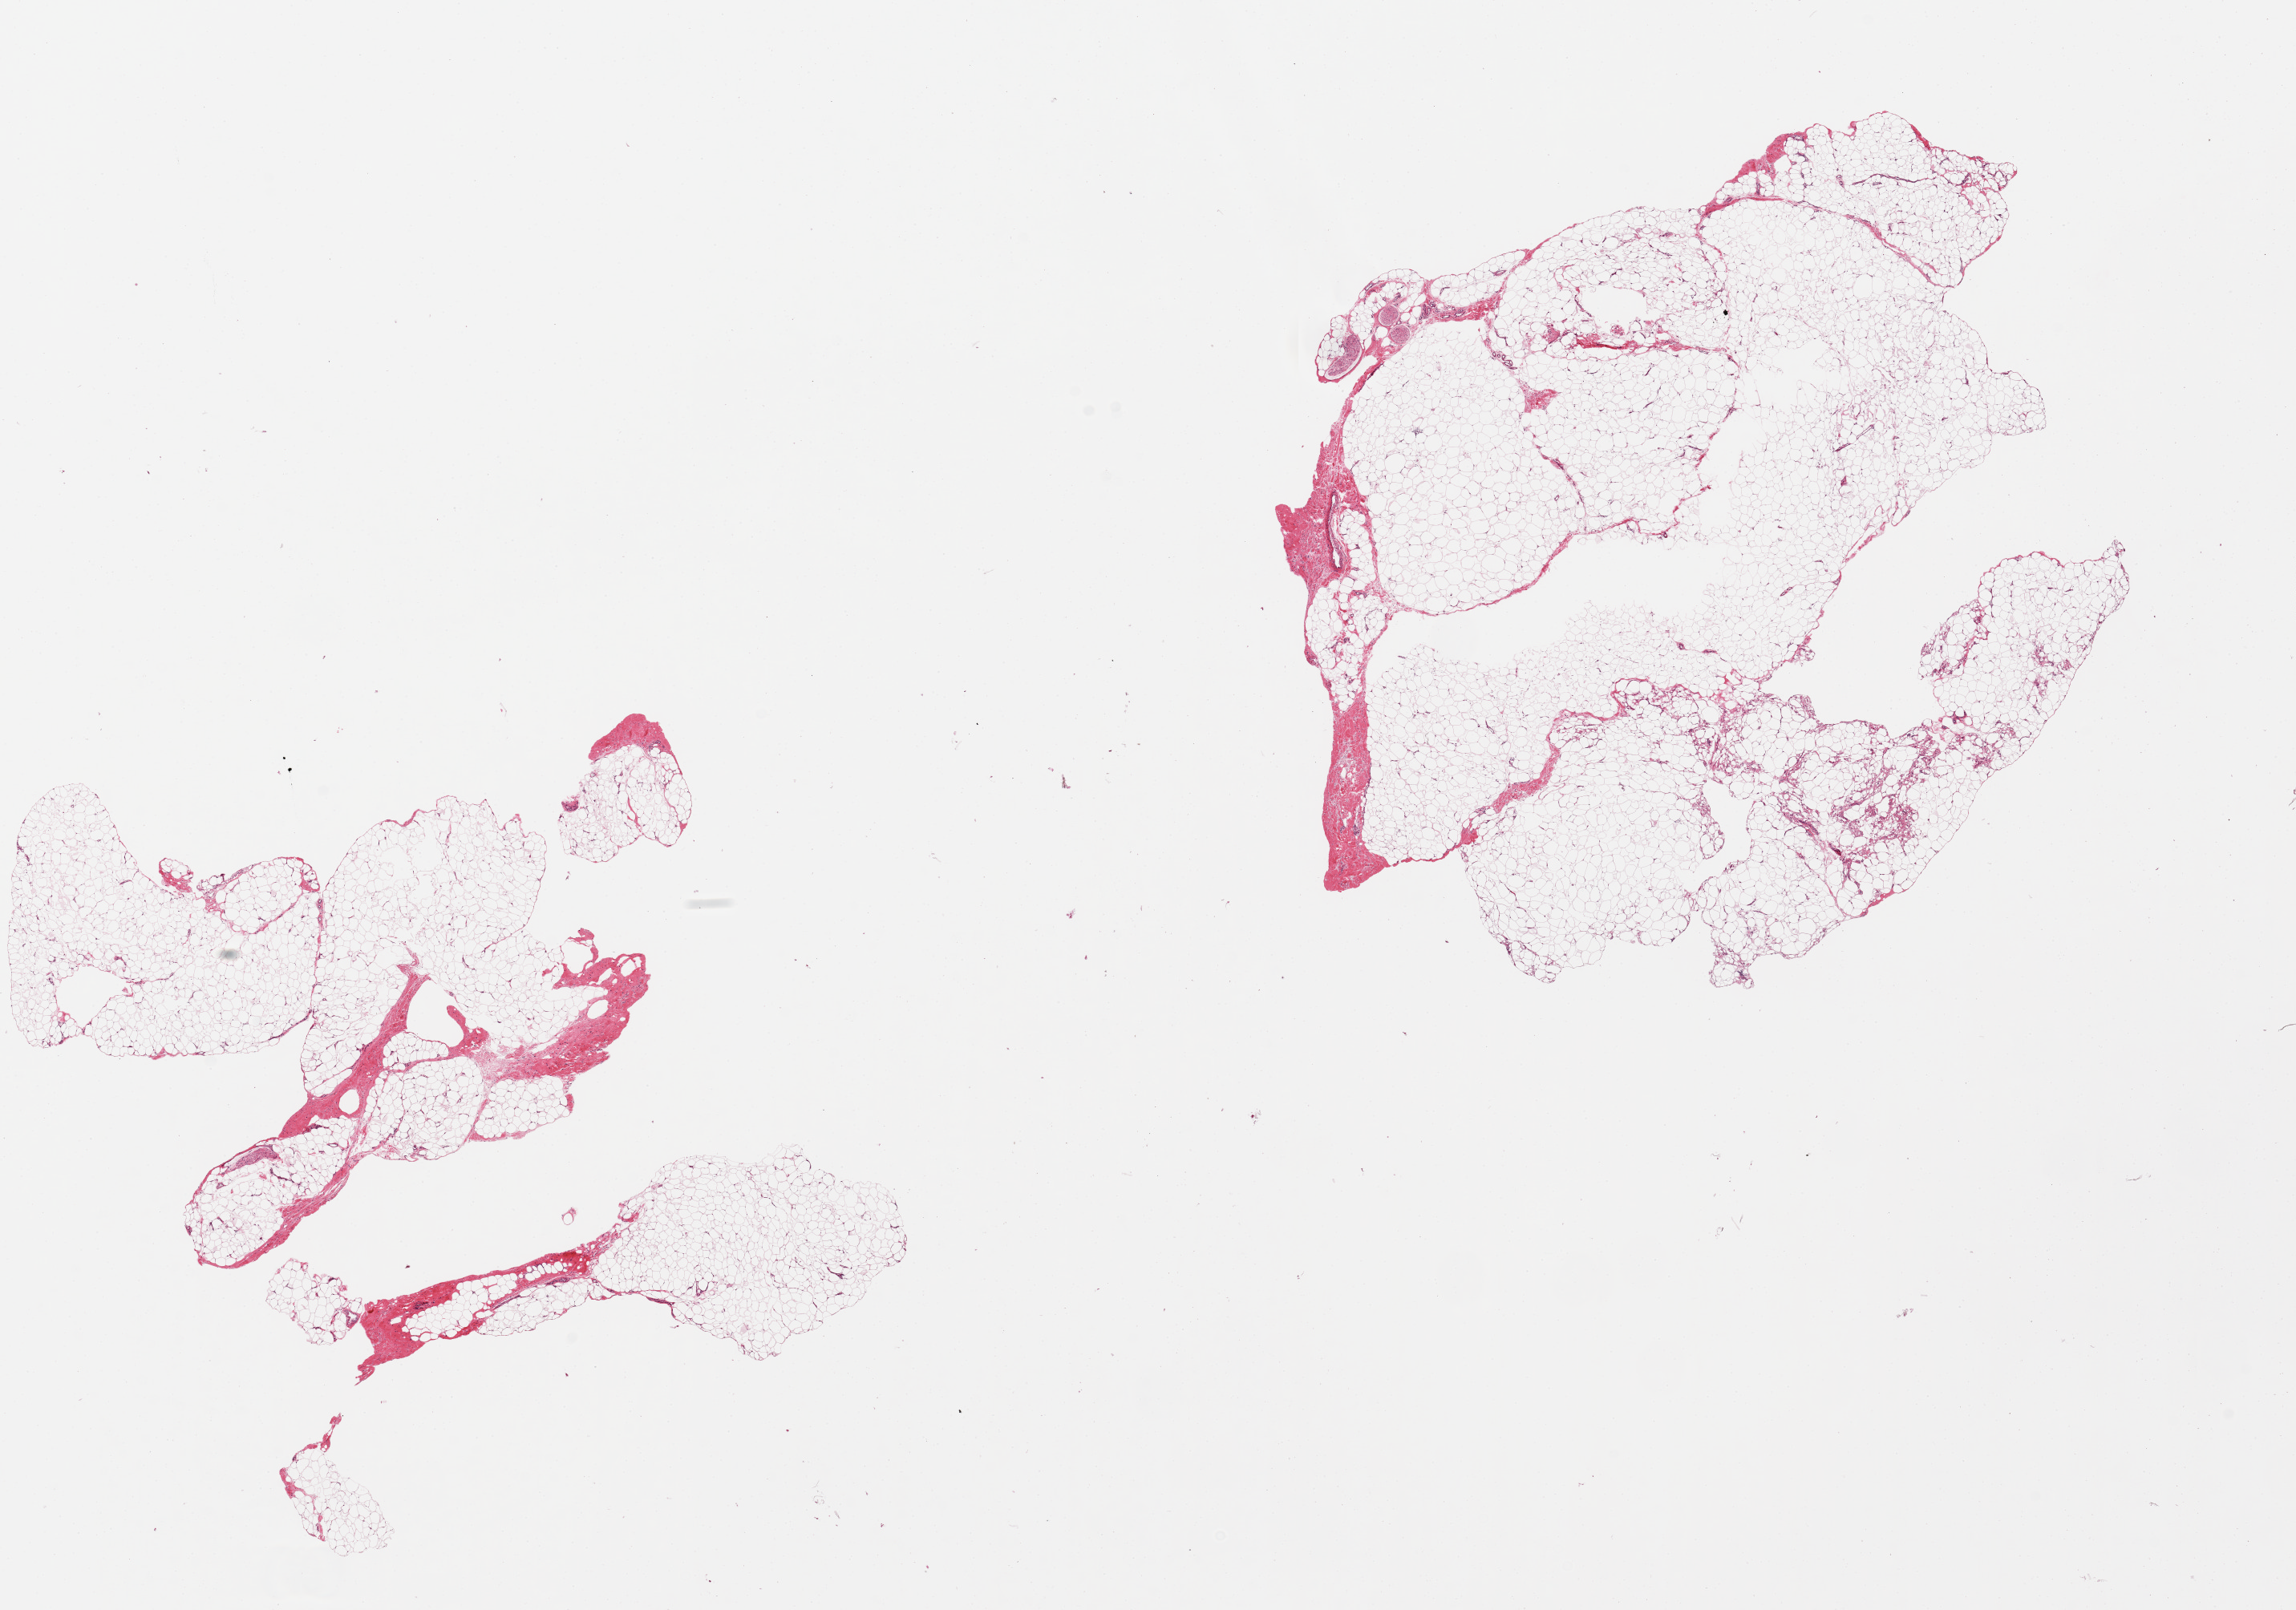
Whole-slide image, hematoxylin and eosin (H&E) stain, low-resolution overview of the scanned area, about 22.6 x 15.9 mm (acquisition: 20x scan). PAXgene-fixed, paraffin-embedded tissue. Target tissue: adipose tissue. Donor tissue sample. Donor: female.
Pathologist's review note for this sample: 2 pieces, ~10% fibrous/fascial tissue.